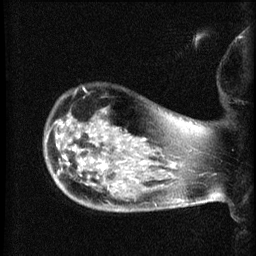
Breast MRI (dynamic contrast-enhanced), one sagittal slice; slice 53 of 60 in the series (ordered by position); dynamic contrast-enhanced series, image 2 of 3 at this slice position (ordered by acquisition); 1.5 T; TE 4.2 ms, TR 8.2 ms; 2.1 mm slice thickness; 256 × 256 image matrix, field of view 180 × 180 mm. Female patient, age 50 years.
Outlined on this slice (semi-automatically segmented with operator editing):
- analysis volume of interest (the breast-tissue region the enhancement analysis was run in; not a lesion): bounding box [x1, y1, x2, y2] px = [44, 96, 169, 211]
- tumour enhancement mask (voxels above the 70 % enhancement threshold inside the analysis volume of interest): [101, 164, 104, 166]